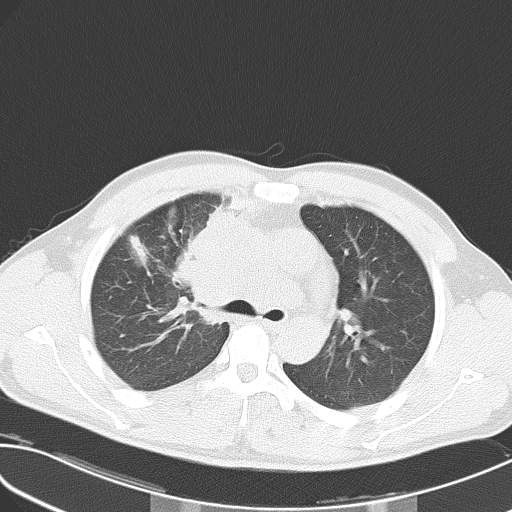
Chest CT, one axial slice. Position 37 of 55 along the scan axis. Reconstruction kernel B70f. 120 kVp. Lung window (W 1500 / L -600 HU). 5 mm slice thickness. 512 × 512 image matrix. Patient: male, 32 years. Case-level facts recorded for this patient, not image findings: clinical TNM (as recorded): T4 N3 M0; histopathological grade: G3.
Structures marked on this image (rectangle marked by the reading radiologist):
- lung tumour (recorded histology: small cell carcinoma): bounding box (x1, y1, x2, y2) in pixels: (170, 209, 232, 329)